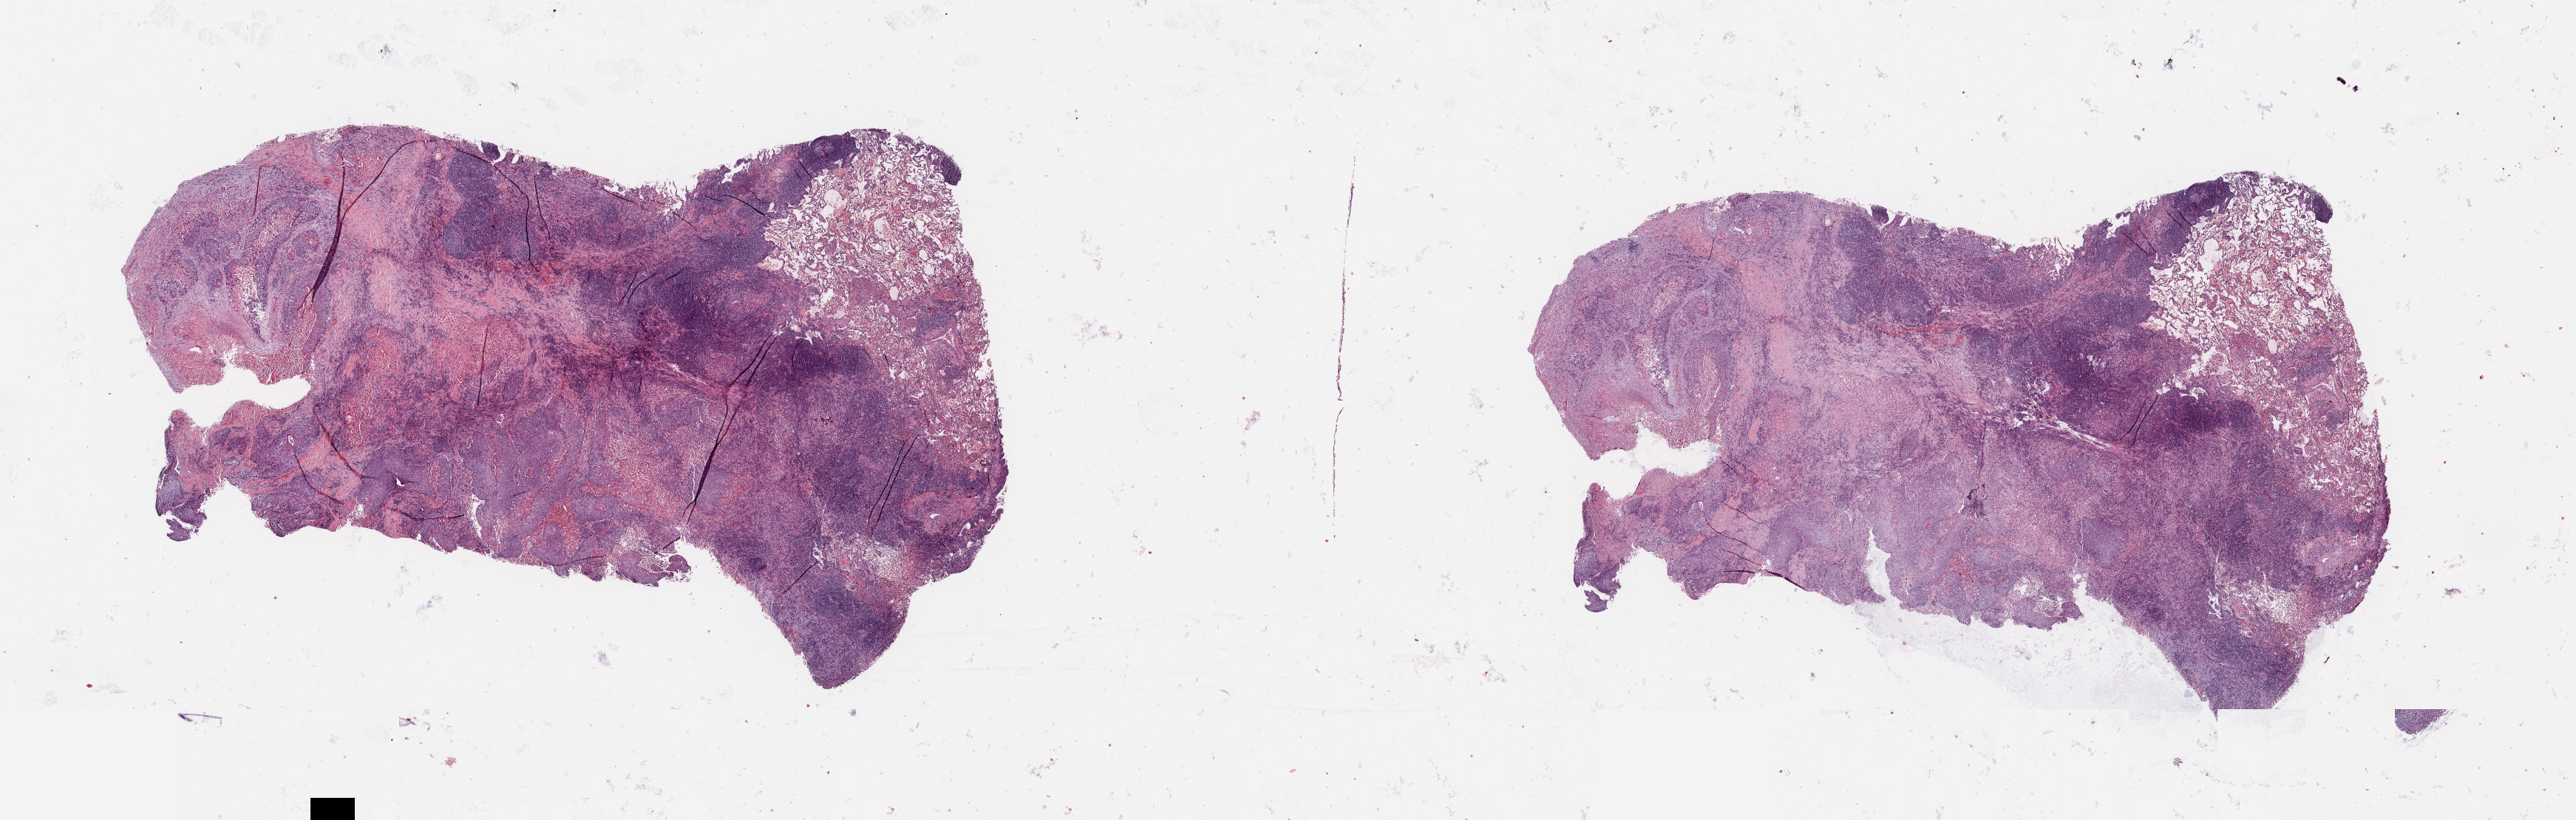
Whole-slide histology image, H&E-stained, low-resolution overview of the scanned area, about 27.6 x 8.8 mm (slide scanned at 20x), tumour tissue sample, lung. Patient: female, age 48 years. Histologic grade: G2 (moderately differentiated).
• diagnosis: Squamous cell carcinoma, NOS
• primary tumour site (as recorded): left upper lobe
• AJCC pathologic stage: IB